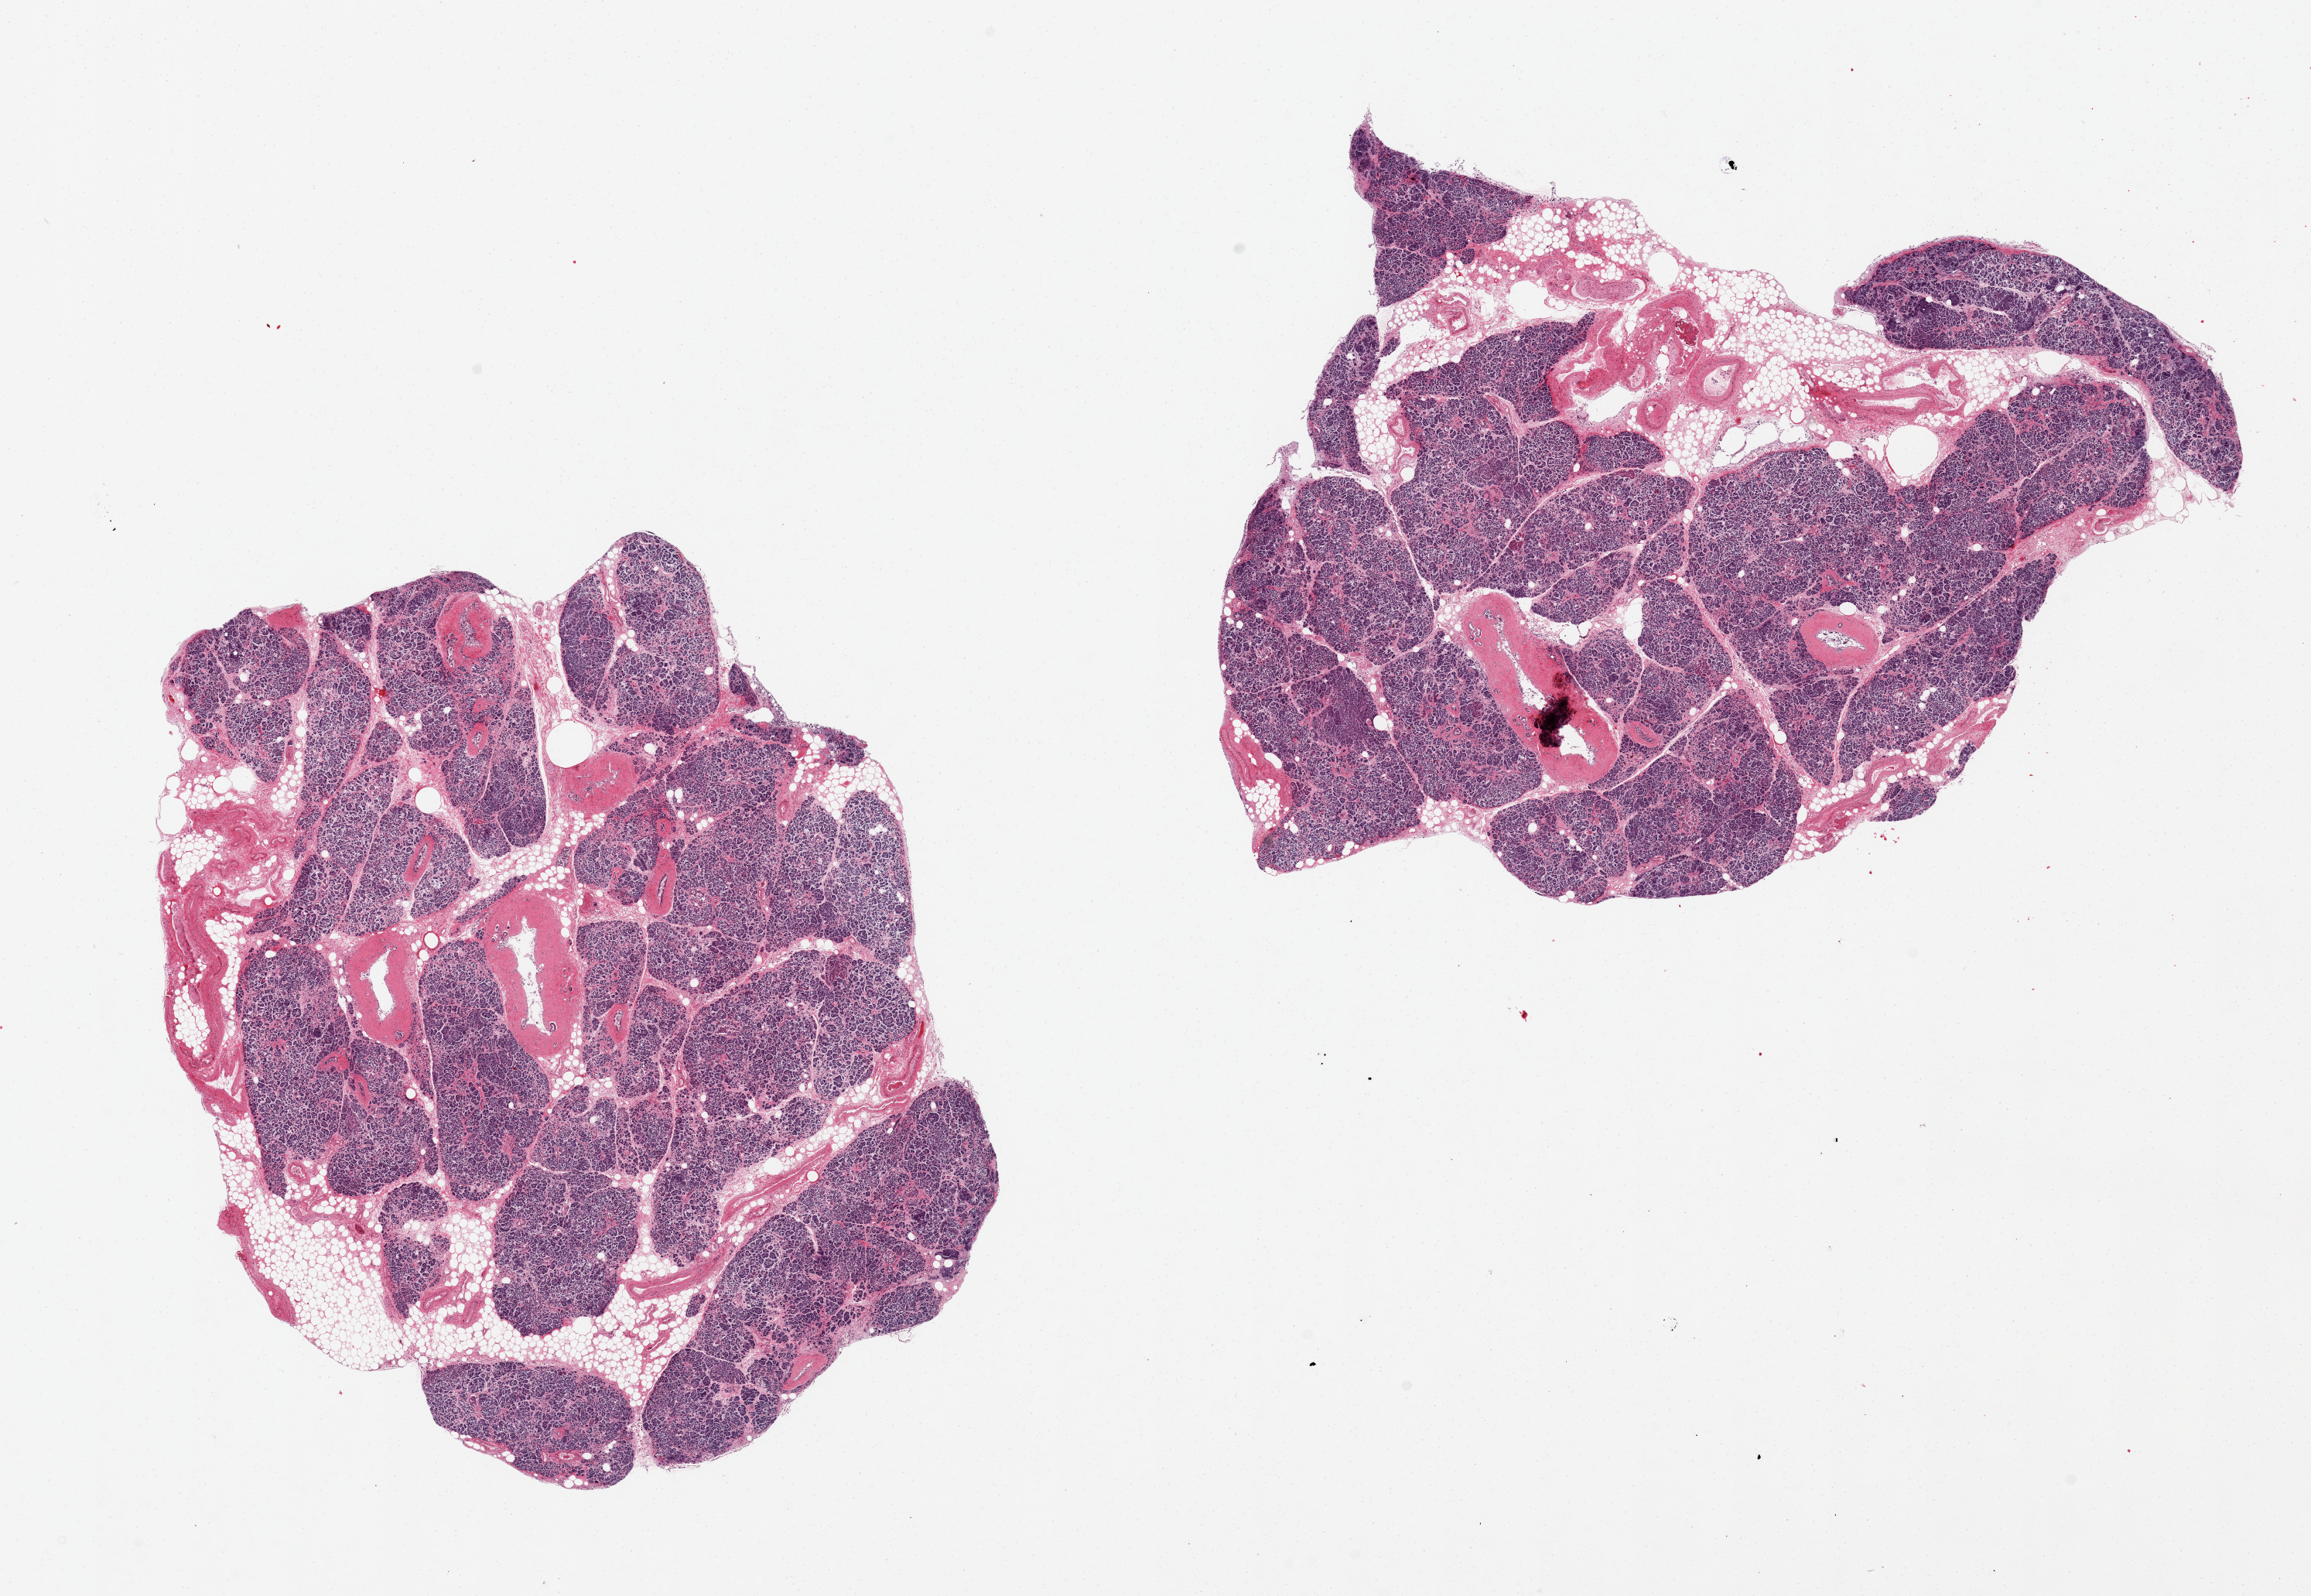
Digitized haematoxylin and eosin-stained section, whole scanned area (about 23.6 x 16.3 mm) shown as a low-resolution overview, PAXgene-fixed paraffin-embedded (PFPE) section, target tissue: pancreas, donor tissue sample.
Review note (as recorded): 2 pieces, mrked autolysis/saponification. An occasional Islet is visible, poorly preserved.